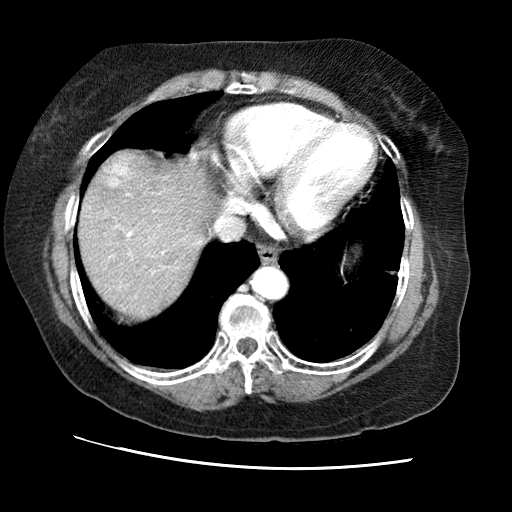
Contrast-enhanced abdominal CT (liver protocol), one axial slice; slice 63 of 65 in the series (ordered by position); reconstruction kernel STANDARD; 120 kVp; soft-tissue window (W 400 / L 40 HU); 512 × 512 image matrix, field of view 340 × 340 mm. Case-level facts recorded for this patient, not image findings: diagnosis: hepatocellular carcinoma (patient treated with transarterial chemoembolisation; whether this scan precedes or follows treatment is not stated here); TNM stage (as recorded): Stage-II; Child-Pugh class: A; tumour differentiation: no biopsy; tumour nodularity: multinodular.
Outlined on this slice (semi-automatically segmented with operator editing):
- liver parenchyma outside the tumour (the mass and vessels are separate outlines, so this box may not span the whole liver): bounding box <78,150,212,317> (left, top, right, bottom; pixels)
- mass: <96,151,140,187>
- liver vessels: <109,154,201,274>